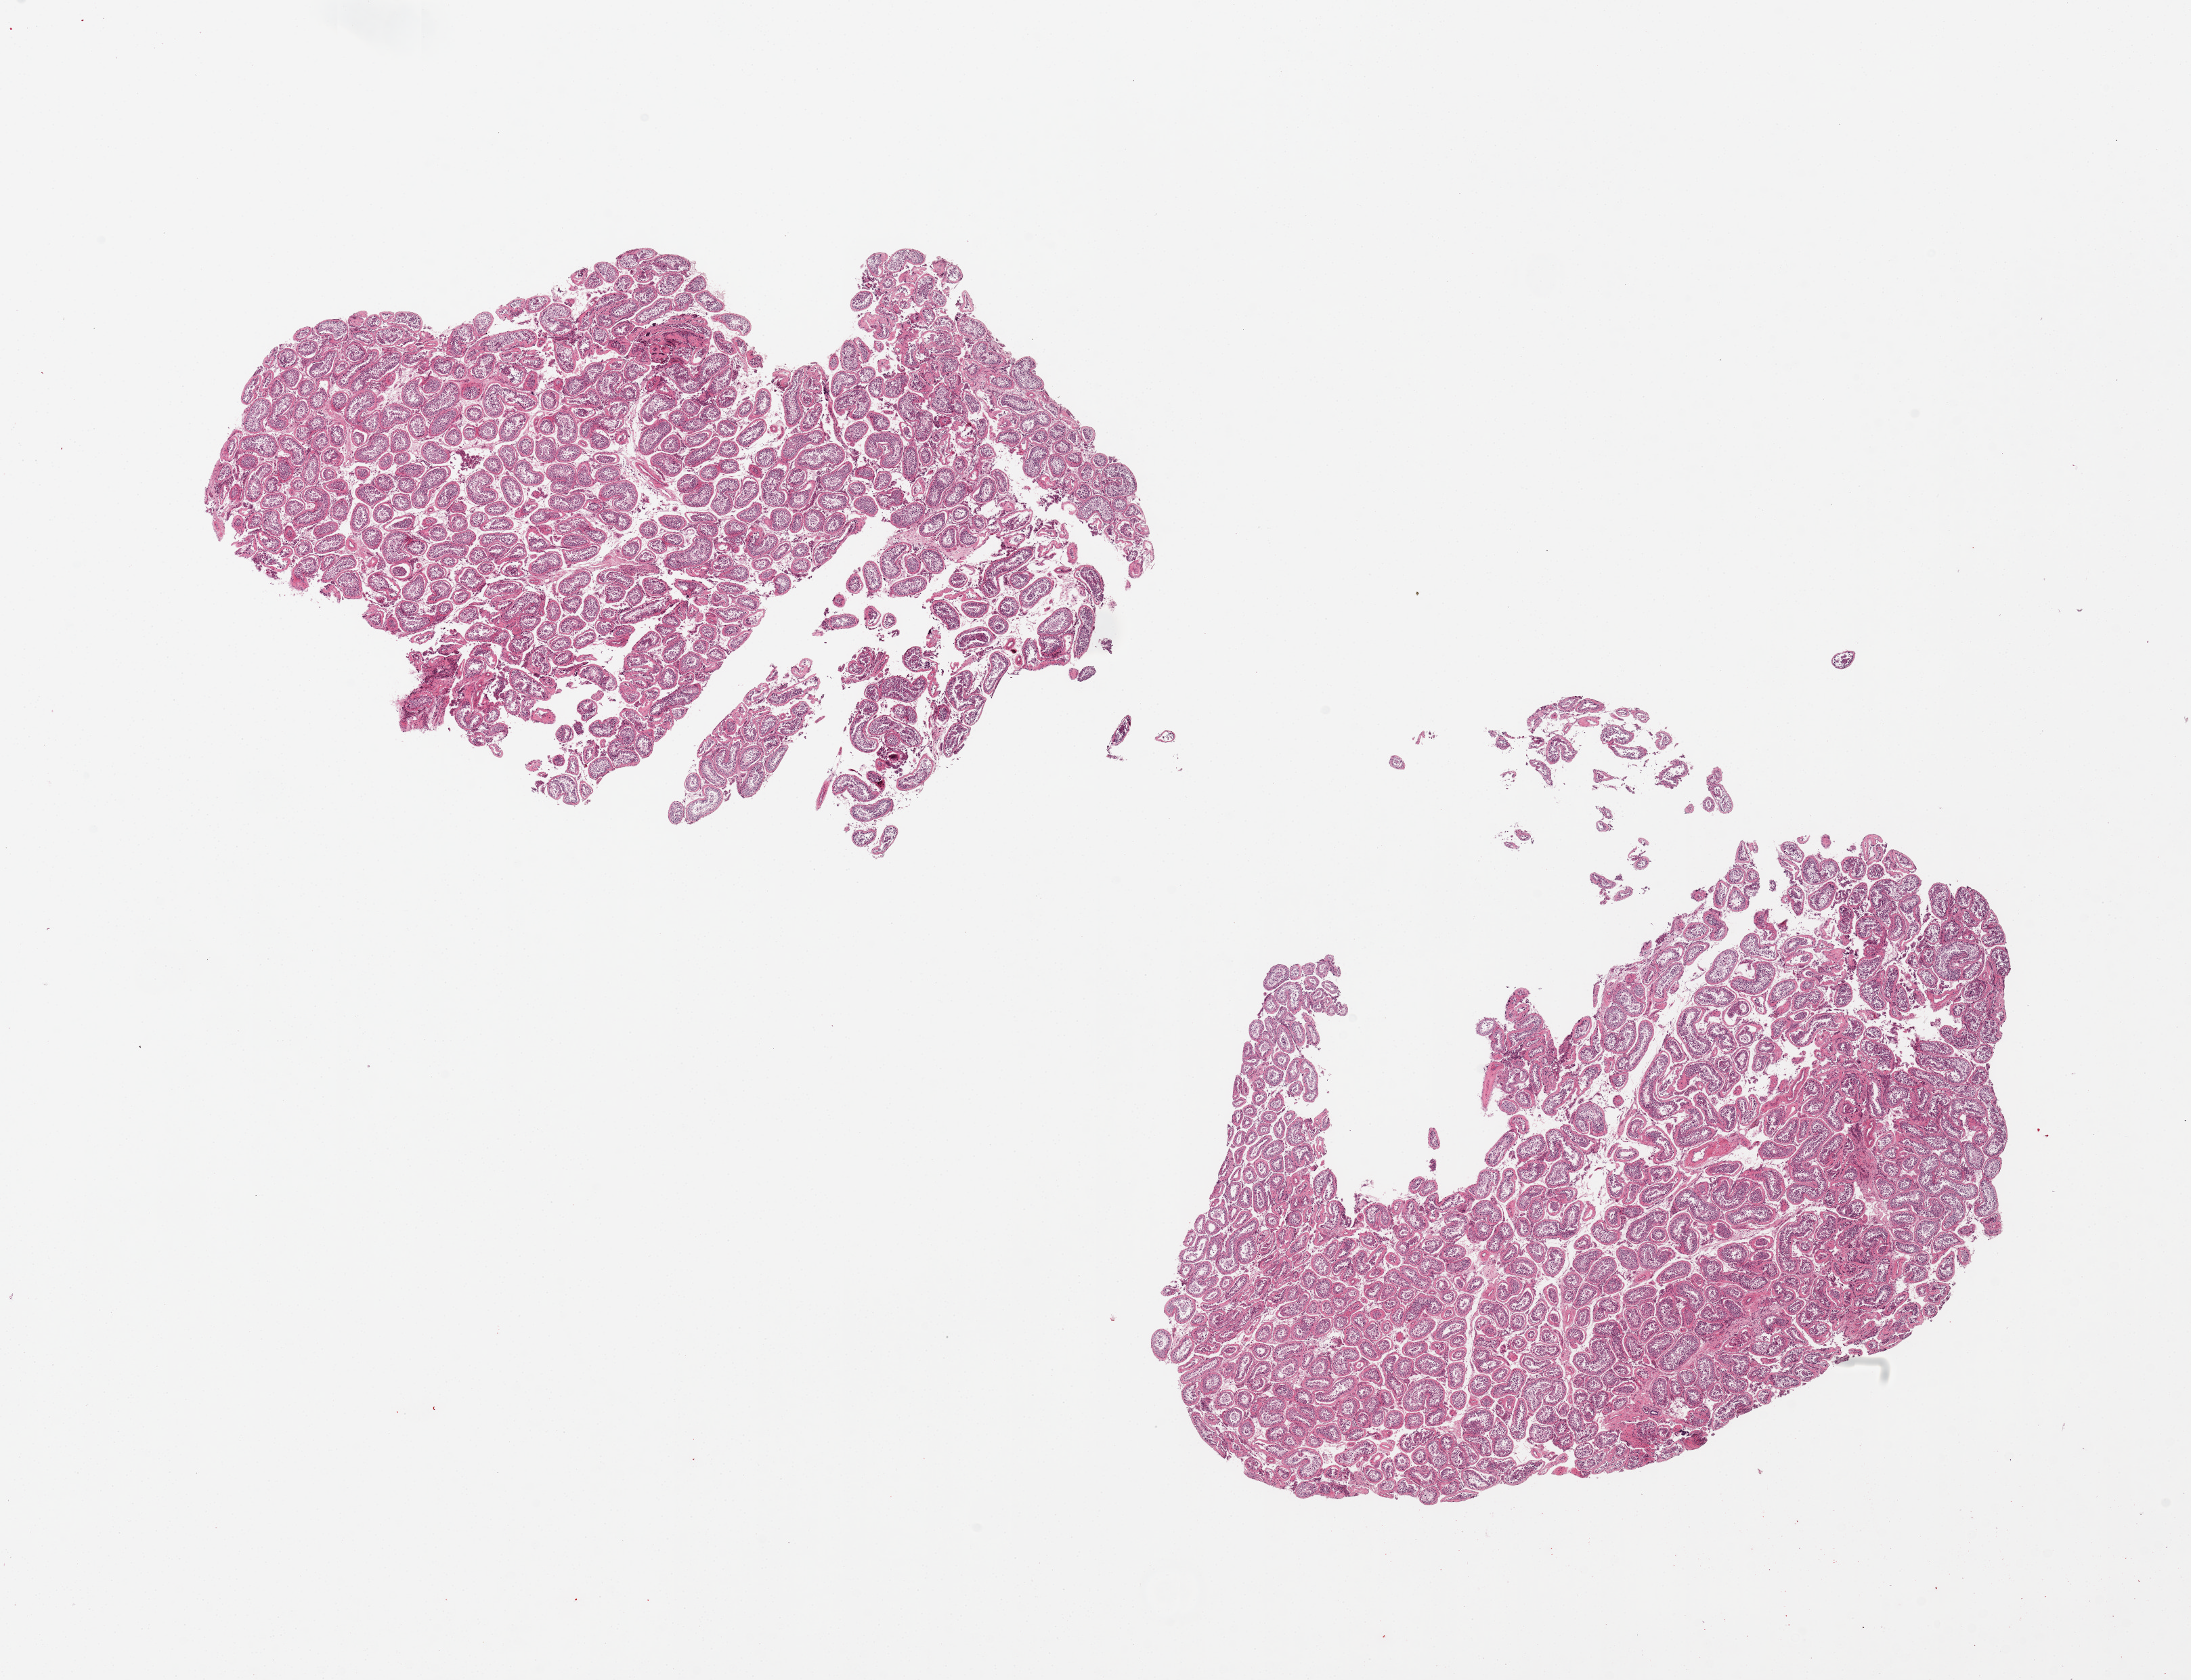
Digitized hematoxylin and eosin (H&E)-stained section, whole scanned area (about 25.6 x 19.6 mm, acquisition: 20x scan) shown as a low-resolution overview. PAXgene-fixed, paraffin-embedded tissue. Sampled site (target tissue): testis. Tissue donor sample. Donor: male.
• pathologist's review note for this sample: 2 pieces, spermatogenesis present